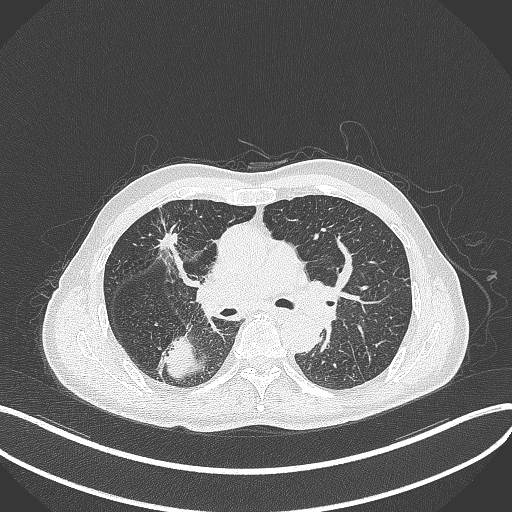
Chest CT, one axial slice; slice 271 of 428 in the series (ordered by position); reconstruction kernel B70f; lung window (W 1500 / L -600 HU); 1 mm slice thickness; 512 × 512 image matrix. Male patient, age 79 years. From the clinical record (not read from this slice): clinical TNM (as recorded): T3 N0 M0.
Structures marked on this image (bounding box drawn by a radiologist):
- lung tumour (recorded histology: adenocarcinoma): bounding box [x1, y1, x2, y2] px = [160, 330, 203, 381]